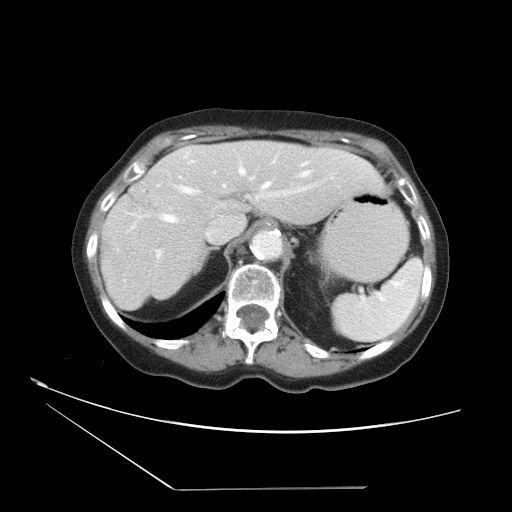
Contrast-enhanced abdominal CT, one axial slice; position 25 of 36 along the scan axis; 120 kVp; soft-tissue window (W 400 / L 40 HU); 5 mm slice thickness; 512 × 512 image matrix. Female patient, age 81 years. Case-level facts recorded for this patient, not image findings: diagnosis: colorectal cancer liver metastases, imaged before liver resection; multiple liver metastases: no; largest metastasis: 1.6 cm; disease in both lobes: no.
Annotated regions visible in this slice (expert manual segmentation):
- hepatic veins: bounding box [x1, y1, x2, y2] px = [160, 160, 313, 223]
- liver: [100, 141, 385, 311]
- planned liver remnant (the part of the liver to remain after resection): [100, 141, 385, 311]
- portal vein (with intrahepatic branches): [158, 178, 311, 256]